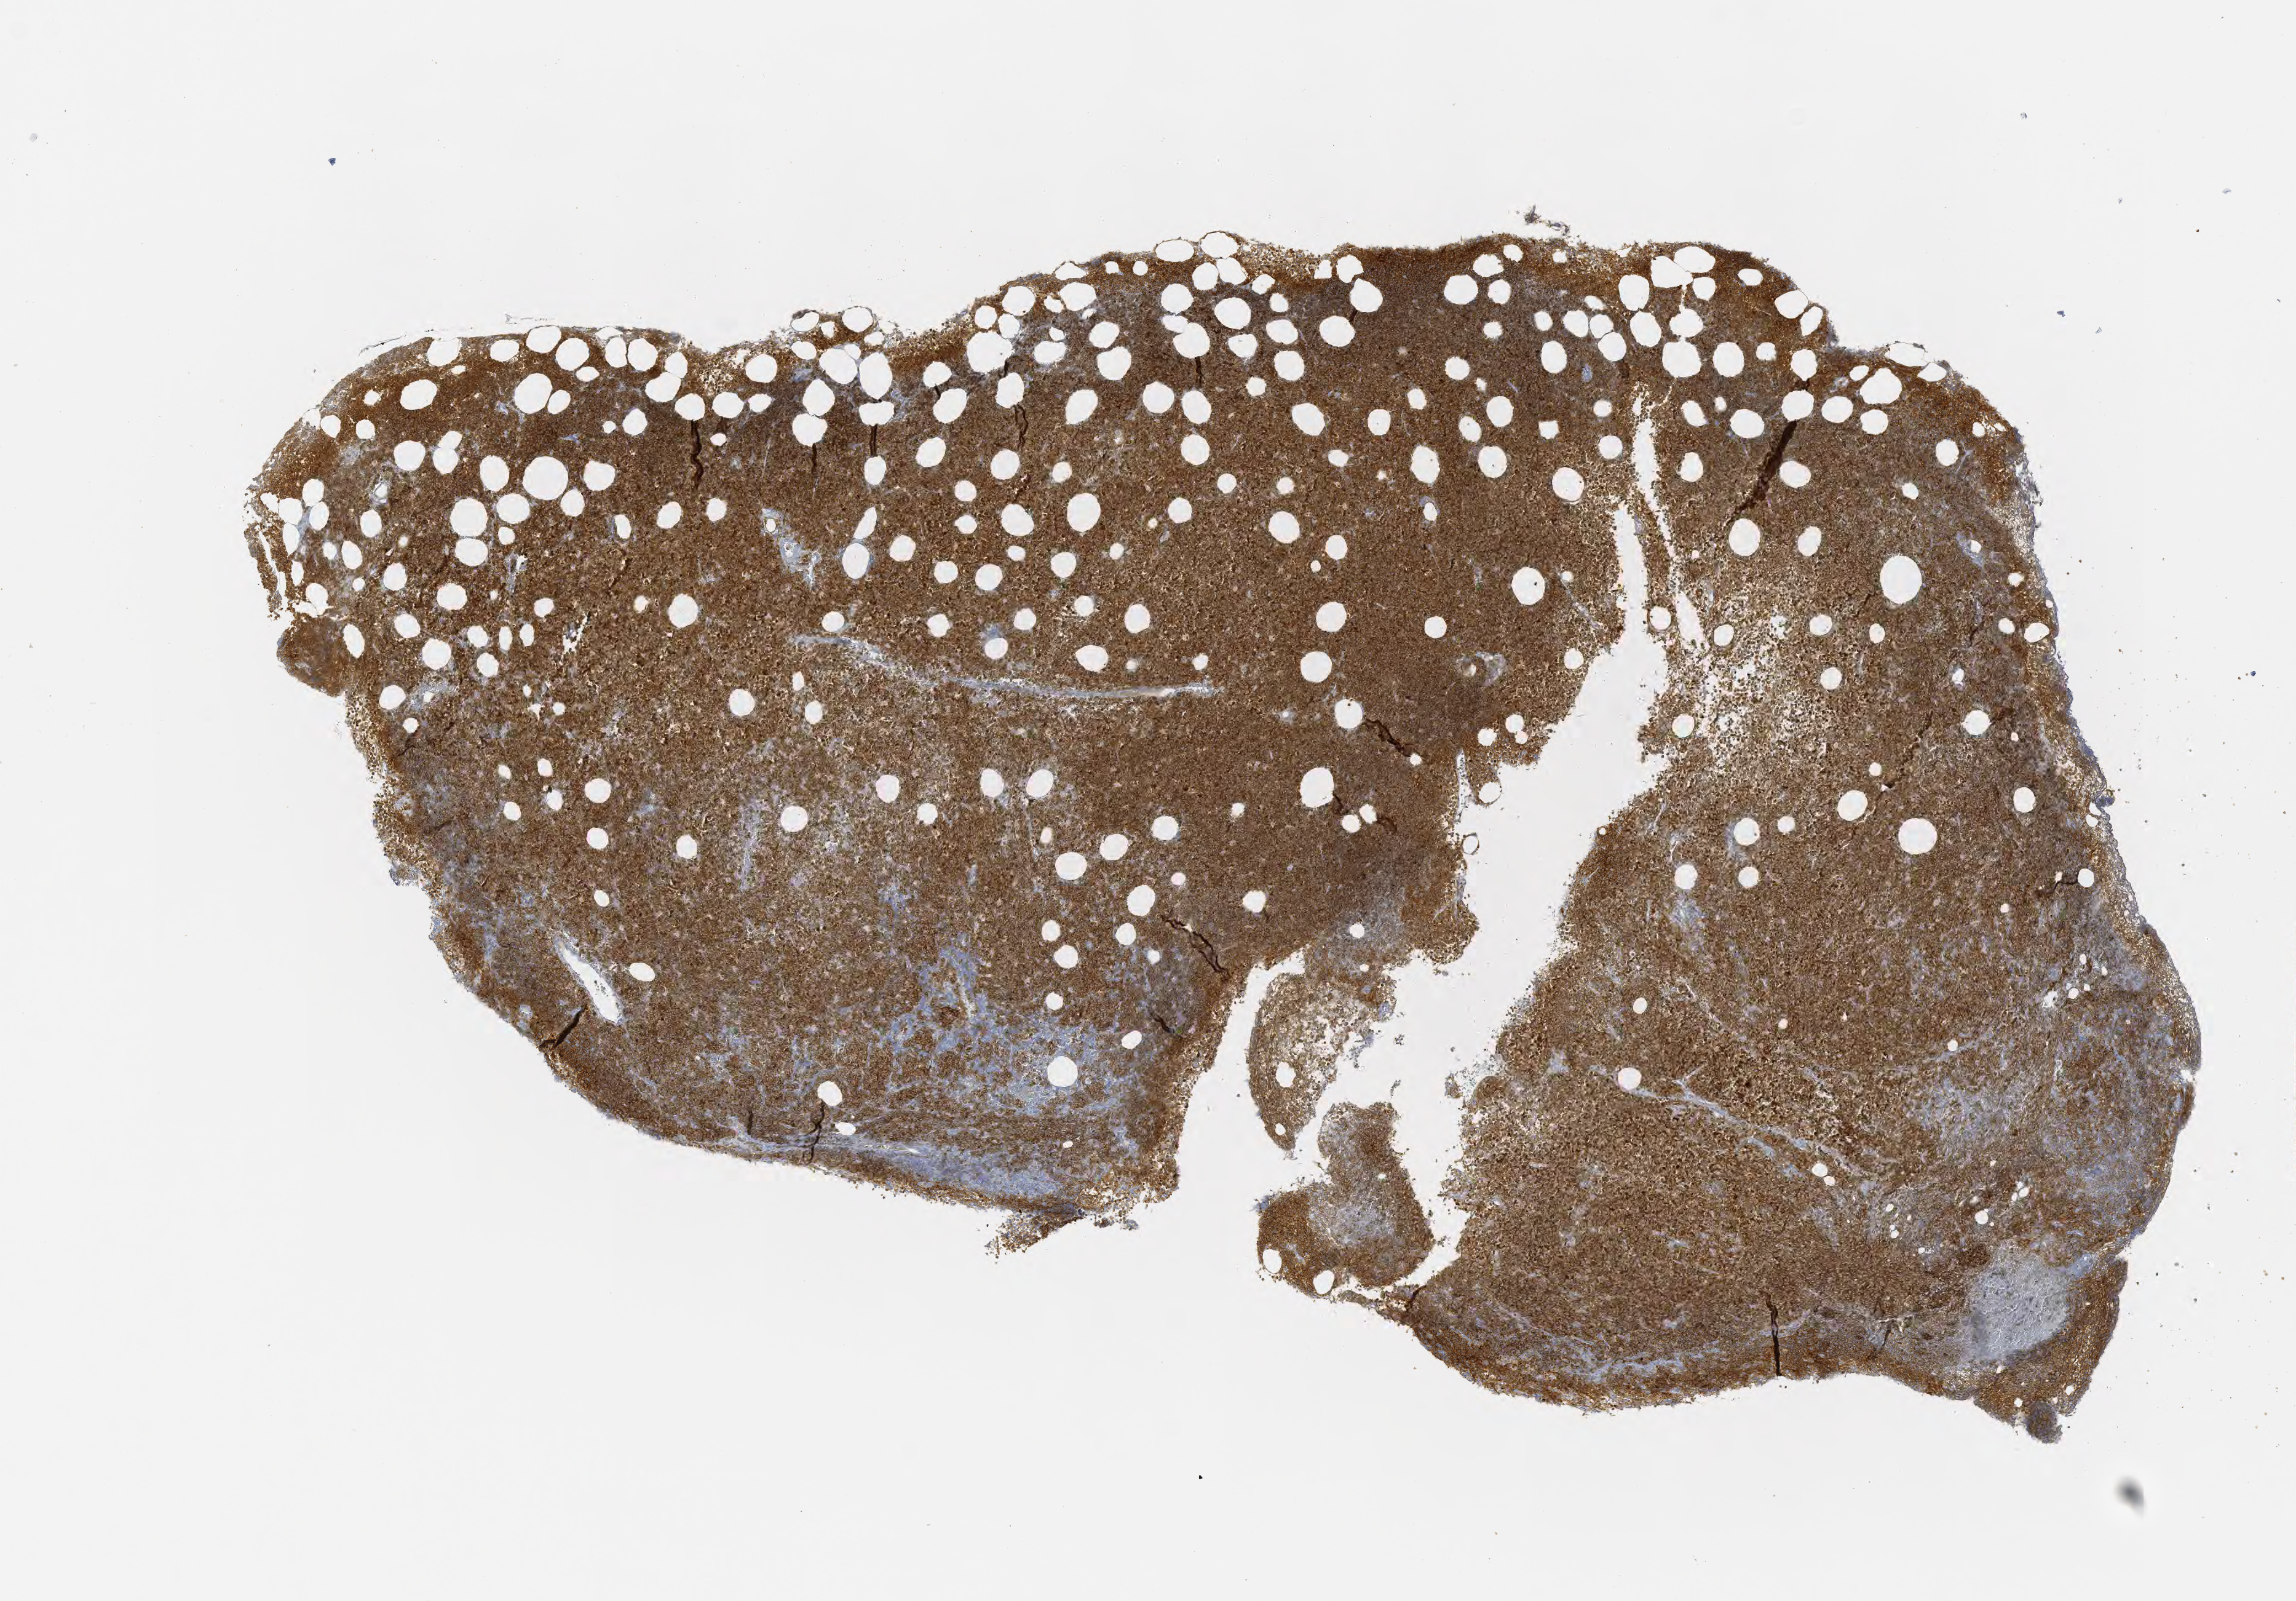
Immunohistochemistry (IHC) whole-slide image stained for CD10 — shown as a low-resolution overview of the whole scanned area (about 7.5 x 5.3 mm); specimen: tumor tissue; anatomic site: bone marrow. Male patient, 70 years old.
Diagnosis: Neoplasm, uncertain whether benign or malignant.